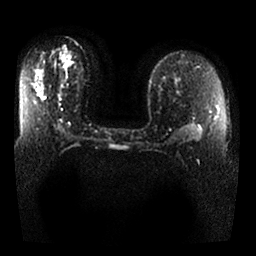
Breast MRI, one axial slice; slice 14 of 25 in the series (ordered by position); diffusion-weighted series; image 2 of 4 stored at this slice position (different b-values; order by instance number); 1.5 T; 256 × 256 image matrix, field of view 340 × 340 mm. Female patient.
Annotated regions visible in this slice (manually delineated by an expert):
- tumour on diffusion-weighted imaging: bounding box <62,55,69,66> (left, top, right, bottom; pixels)